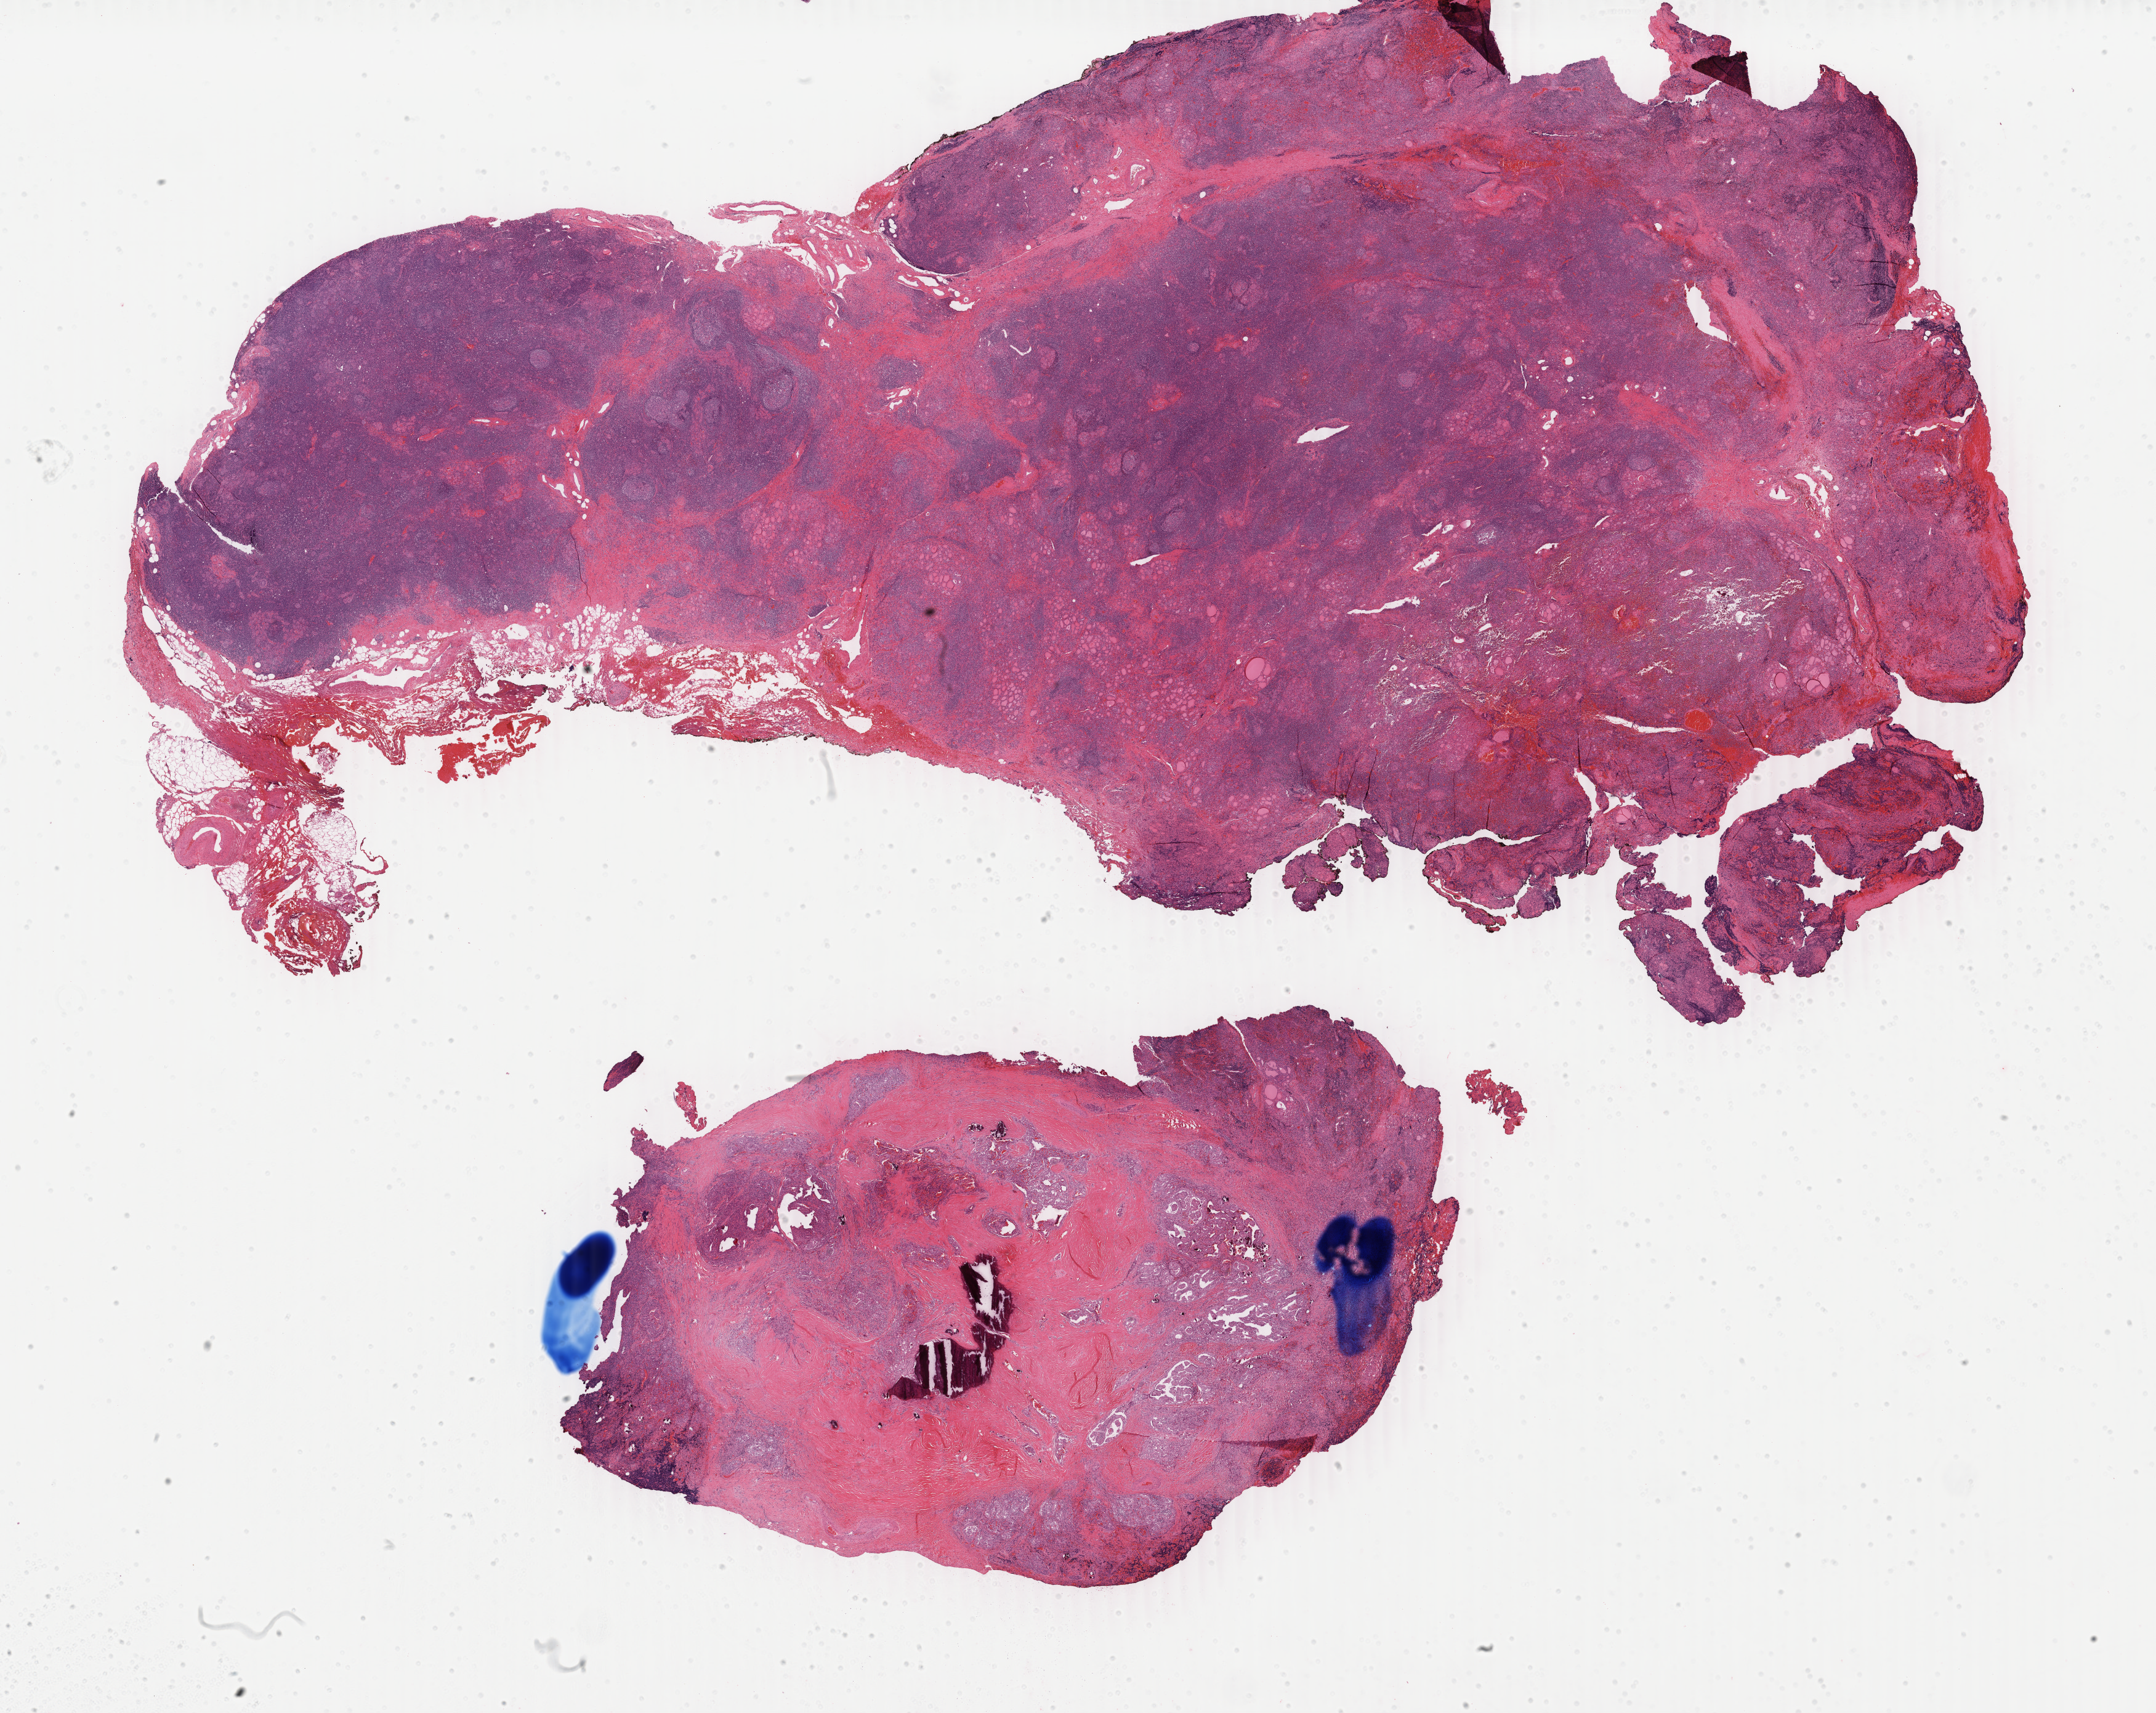
Digitized H&E tissue section (whole slide) — shown as a low-resolution overview of the whole scanned area (about 27.8 x 22.1 mm), formalin-fixed paraffin-embedded (FFPE) diagnostic section, thyroid, primary tumour sample. Patient: female, age at initial diagnosis 46 years.
• lymph nodes positive (case pathology): 1 of 16 examined
• AJCC pathologic stage: III
• diagnosis: Papillary adenocarcinoma, NOS